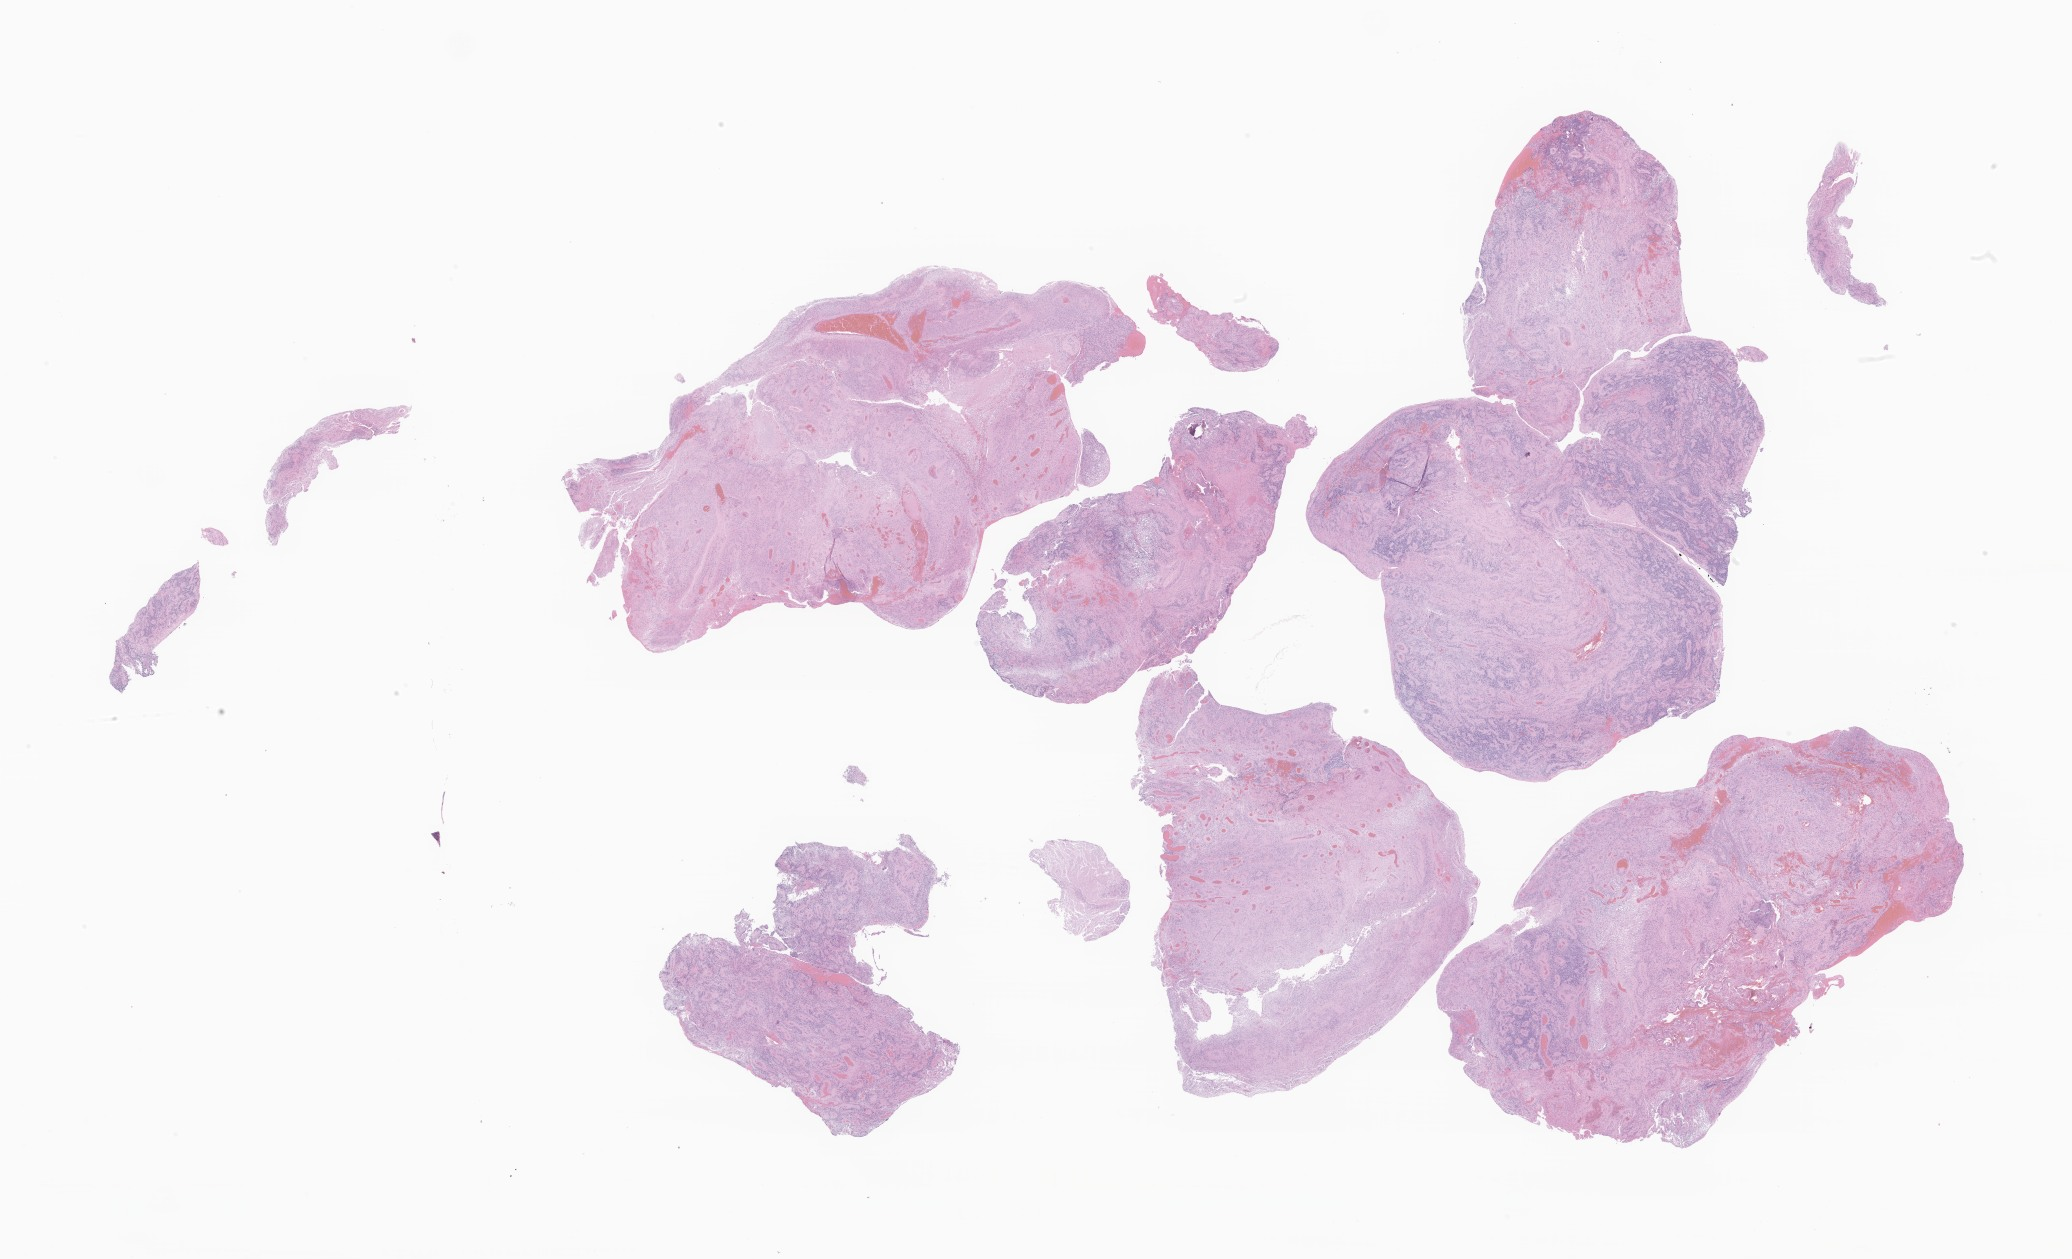
Haematoxylin and eosin whole-slide image of tumor tissue from the brain — whole scanned area (about 35.0 x 21.2 mm) shown as a low-resolution overview. Female patient, age 851 days (about 2.3 years).
Specimen: formalin-fixed, paraffin-embedded (FFPE) tissue.